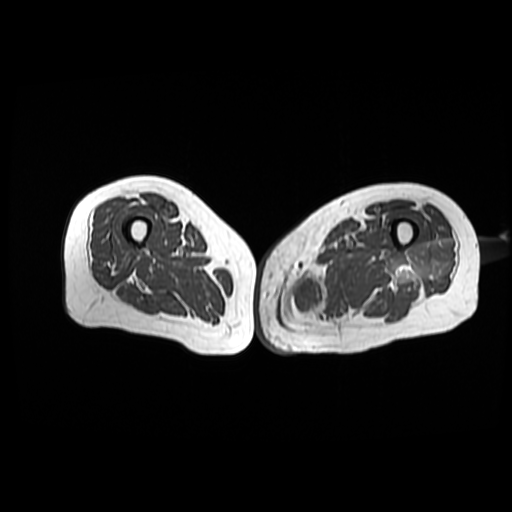
MRI of an extremity soft-tissue mass, one axial slice. Position 40 of 42 along the scan axis. 6 mm slice thickness. 512 × 512 image matrix, field of view 420 × 420 mm. Female patient. Case-level facts recorded for this patient, not image findings: histological type: pleomorphic leiomyosarcoma; grade: high; site of the primary tumour: left thigh.
Structures marked on this image (expert manual segmentation):
- gross tumour volume including surrounding oedema: bounding box (x1, y1, x2, y2) in pixels: (285, 266, 355, 327)